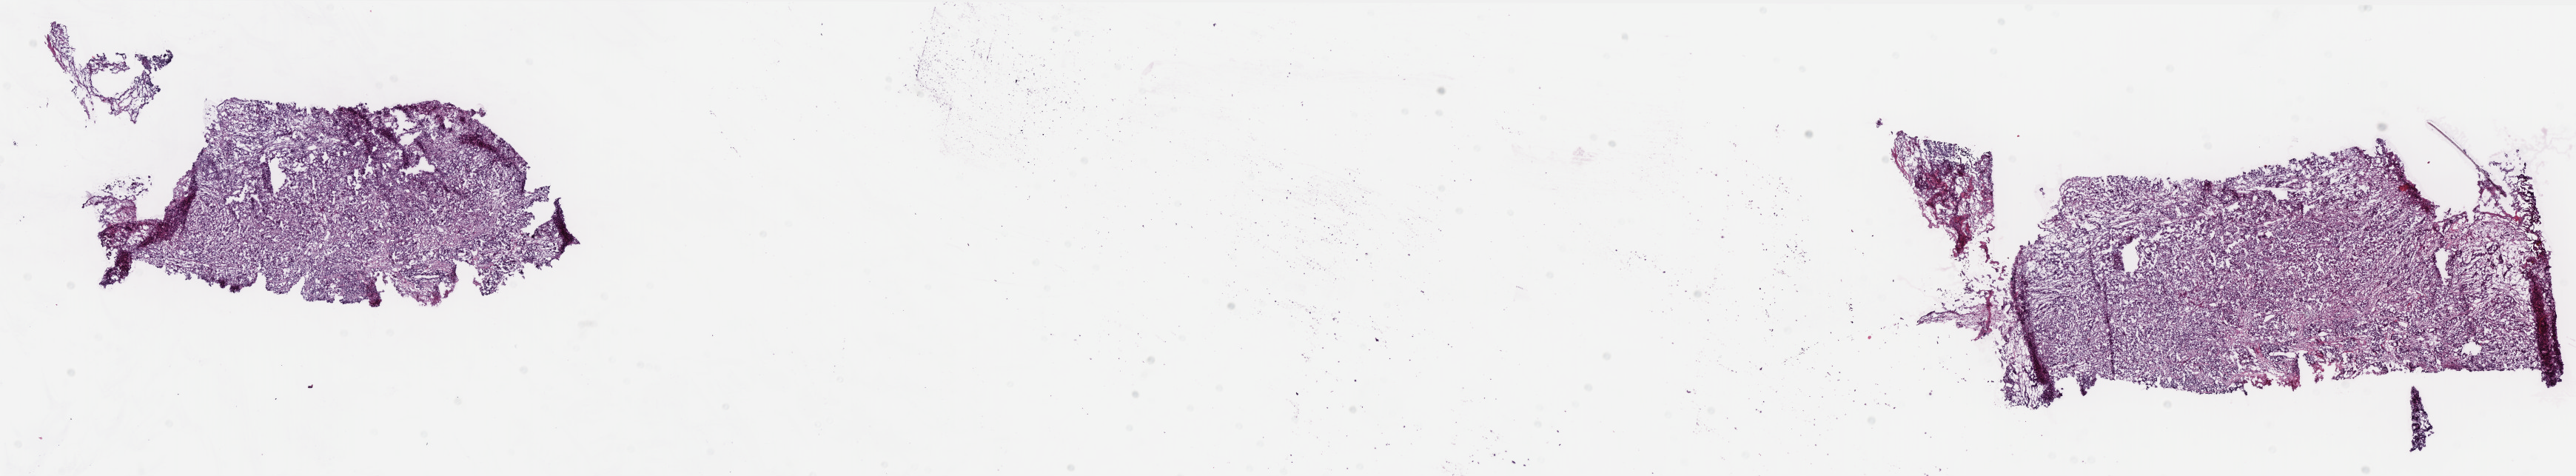
Whole-slide histology image, H&E-stained — shown as a low-resolution overview of the whole scanned area (about 27.9 x 5.2 mm). Frozen section. Uterus, primary tumour sample. Female patient; age at initial diagnosis 64 years. Histologic grade: G3 (poorly differentiated). Pathologist review of this section (percent, as recorded): tumour cells 72%, tumour nuclei 88%, normal cells 0%, stromal cells 25%, necrosis 3%. Inflammatory infiltration, as recorded: lymphocyte infiltration 1%, monocyte infiltration 0%, neutrophil infiltration 0%.
• lymph nodes positive (case pathology): 0 of 20 examined
• histologic diagnosis: Endometrioid adenocarcinoma, NOS
• FIGO stage: II